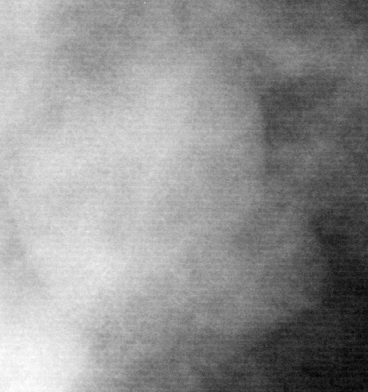
Cropped region of a digitized screen-film mammogram centred on a radiologist-marked abnormality, right breast, CC view, BI-RADS breast density category 2 (scale 1–4).
- Finding: mass, shape lobulated, margins circumscribed; BI-RADS assessment category 3; pathology (as recorded): benign.